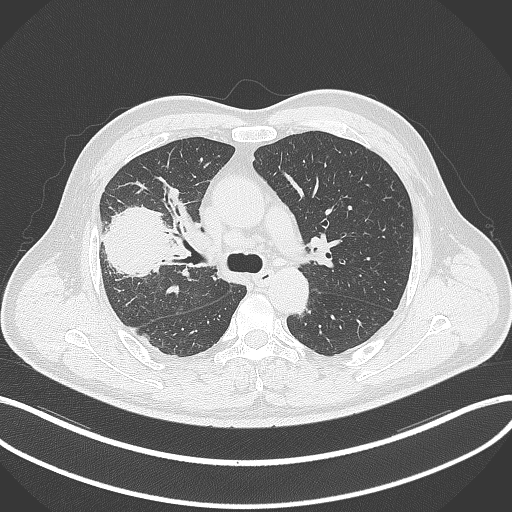
Chest CT, one axial slice; position 218 of 348 along the scan axis; reconstruction kernel B70f; 120 kVp; lung window (W 1500 / L -600 HU); 1 mm slice thickness; 512 × 512 image matrix. Patient: male, 55 years. From the clinical record (not read from this slice): clinical TNM (as recorded): T3 N2 M1.
Structures marked on this image (rectangle marked by the reading radiologist):
- lung tumour (recorded histology: adenocarcinoma): bounding box (x1, y1, x2, y2) in pixels: (98, 203, 177, 279)